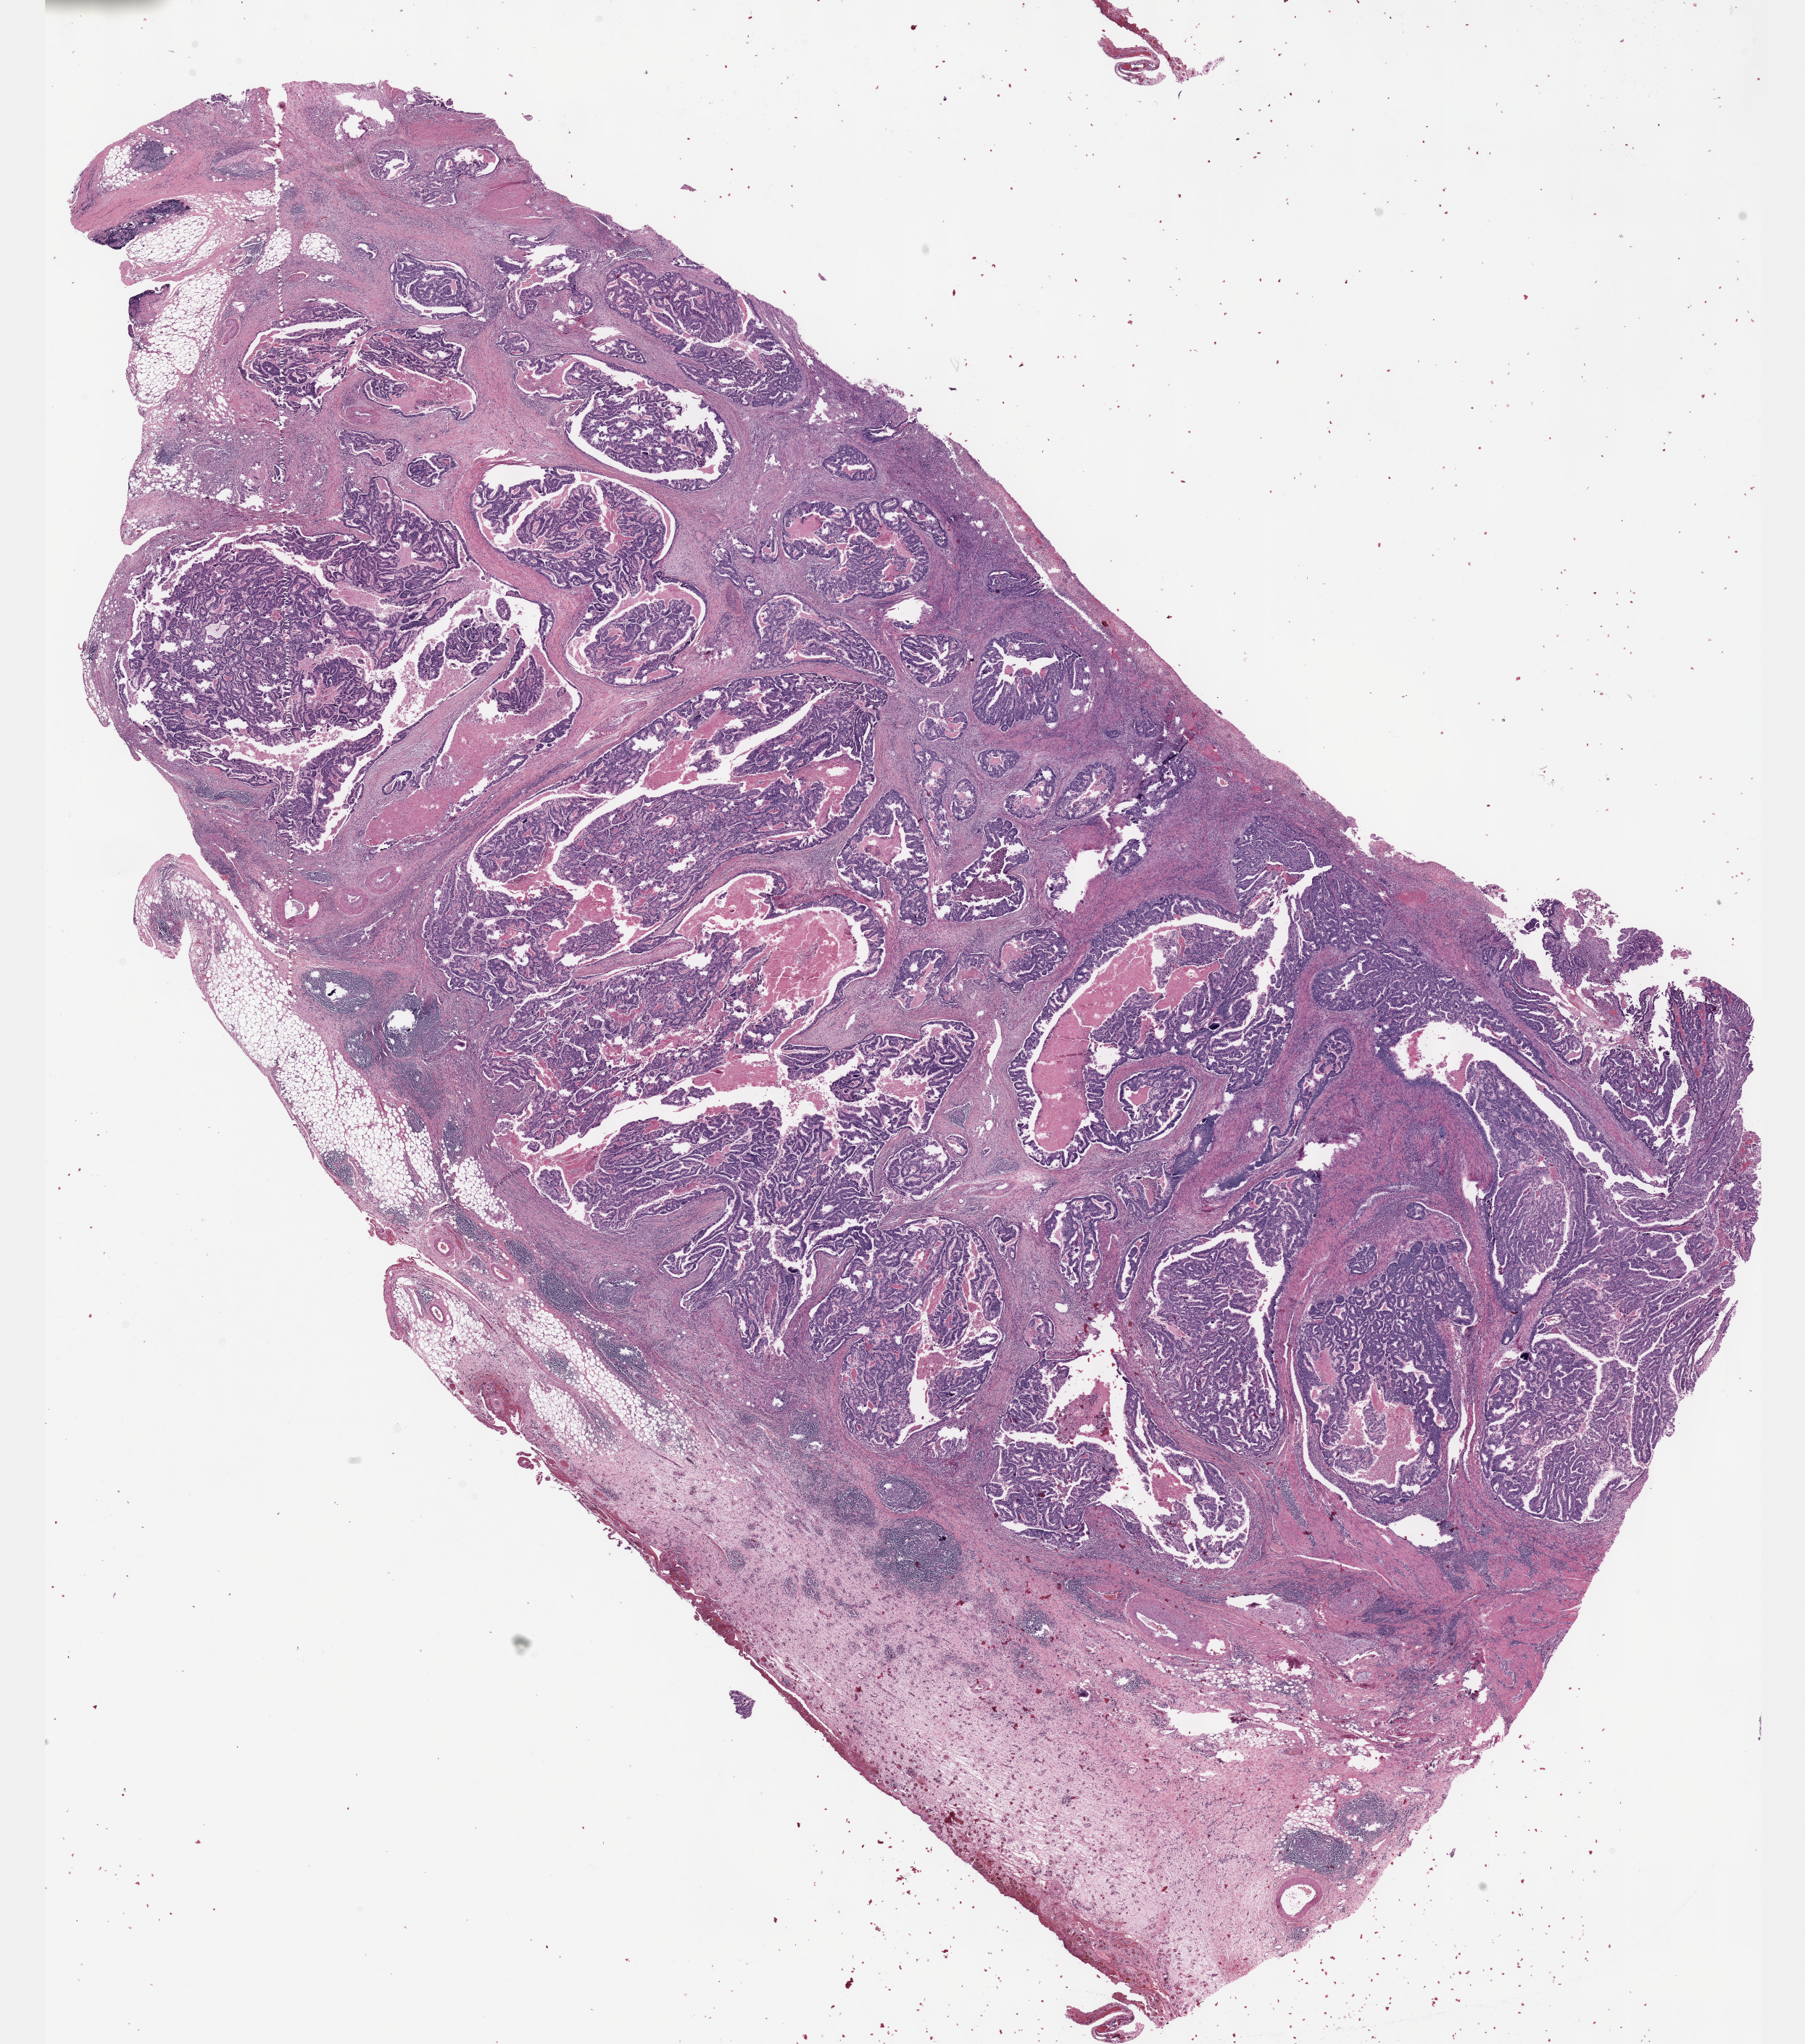
H&E whole-slide image — shown as a low-resolution overview of the whole scanned area (about 20.1 x 22.8 mm); formalin-fixed paraffin-embedded (FFPE) diagnostic section; stomach, primary tumour sample. Patient: male, age at initial diagnosis 74 years. Histologic grade: G2 (moderately differentiated).
AJCC pathologic stage: IIIC (7th edition). Histologic diagnosis: Adenocarcinoma, intestinal type (gastric antrum).